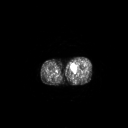
FDG PET of an extremity soft-tissue mass (from a PET/CT study), one axial slice. Slice 227 of 267 in the series (ordered by position). 3.27 mm slice thickness. 128 × 128 image matrix, field of view 700 × 700 mm. Male patient, age 48 years. Case-level facts recorded for this patient, not image findings: histological type: pleiomorphic leiomyosarcoma; grade: high; site of the primary tumour: left thigh.
Outlined on this slice (expert contour drawn on MRI and transferred to this co-registered scan by the dataset authors):
- gross tumour volume including surrounding oedema: box from (x=69, y=63) to (x=76, y=71) px
- gross tumour volume (mass): (x=70, y=64)–(x=75, y=70)